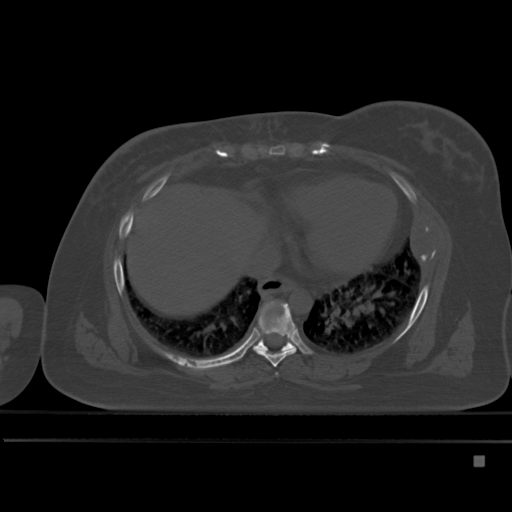
CT including the spine, one axial slice. Slice 286 of 495 in the series (ordered by position). Bone window (W 1800 / L 400 HU). 512 × 512 image matrix, field of view 404 × 404 mm. Female patient, age 33 years. From the clinical record (not read from this slice): primary cancer: breast.
Annotated regions visible in this slice (semi-automatic segmentation, software-assisted and operator-edited):
- T7 vertebra: bounding box [x1, y1, x2, y2] px = [254, 306, 297, 367]
- T8 vertebra: [250, 304, 295, 352]